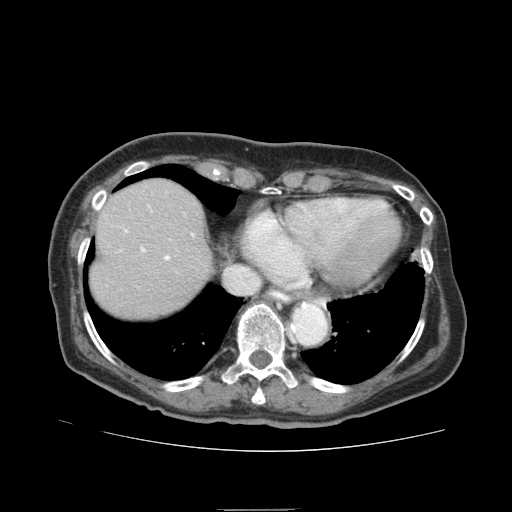
Contrast-enhanced abdominal CT (liver protocol), one axial slice. Slice 72 of 95 in the series (ordered by position). Soft-tissue window (W 400 / L 40 HU). 512 × 512 image matrix, field of view 360 × 360 mm. Case-level facts recorded for this patient, not image findings: diagnosis: hepatocellular carcinoma (patient treated with transarterial chemoembolisation; whether this scan precedes or follows treatment is not stated here); TNM stage (as recorded): Stage-IVA; Child-Pugh class: B.
Outlined on this slice (semi-automatically segmented with operator editing):
- liver parenchyma outside the tumour (the mass and vessels are separate outlines, so this box may not span the whole liver): bounding box [x1, y1, x2, y2] px = [90, 178, 212, 318]
- liver vessels: [124, 229, 194, 261]